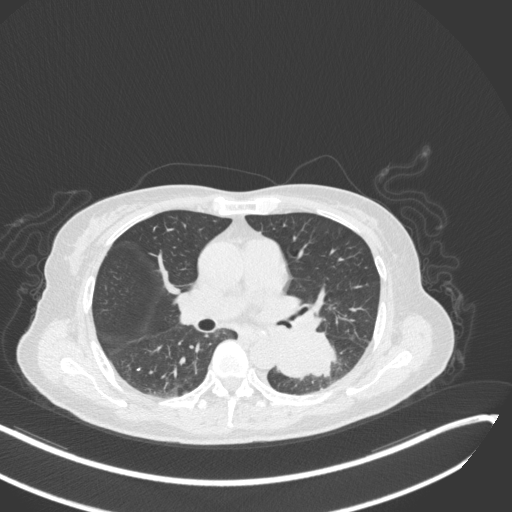
Chest CT, one axial slice. Position 154 of 342 along the scan axis. Reconstruction kernel B31f. Lung window (W 1500 / L -600 HU). 512 × 512 image matrix, field of view 400 × 400 mm. Patient: female, 64 years. Case-level facts recorded for this patient, not image findings: clinical TNM (as recorded): T3 N1 M1; histopathological grade: G3.
Structures marked on this image (rectangle marked by the reading radiologist):
- lung tumour (recorded histology: small cell carcinoma): bounding box <276,329,337,381> (left, top, right, bottom; pixels)